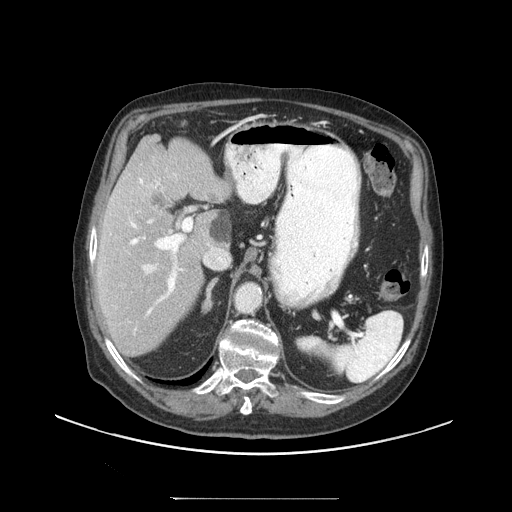
Contrast-enhanced abdominal CT (liver protocol), one axial slice. Slice 64 of 97 in the series (ordered by position). Reconstruction kernel STANDARD. 140 kVp. Soft-tissue window (W 400 / L 40 HU). 2.5 mm slice thickness. 512 × 512 image matrix, field of view 450 × 450 mm. Case-level facts recorded for this patient, not image findings: diagnosis: hepatocellular carcinoma (patient treated with transarterial chemoembolisation; whether this scan precedes or follows treatment is not stated here); TNM stage (as recorded): Stage-IIIC; Child-Pugh class: A; tumour differentiation: well differentiated.
Annotated regions visible in this slice (semi-automatically segmented with operator editing):
- liver parenchyma outside the tumour (the mass and vessels are separate outlines, so this box may not span the whole liver): box from (x=96, y=134) to (x=230, y=356) px
- liver vessels: (x=98, y=174)–(x=209, y=315)